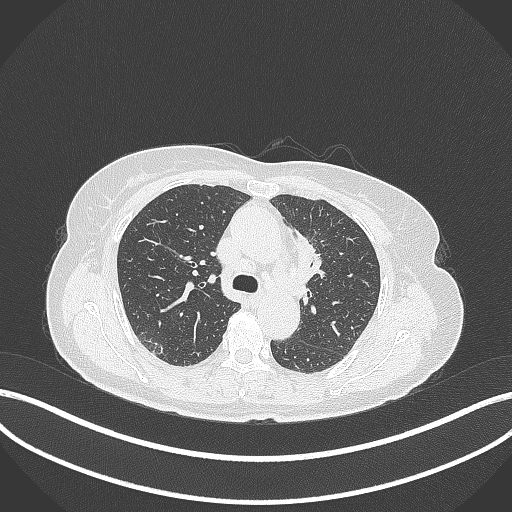
Chest CT, one axial slice. Slice 227 of 369 in the series (ordered by position). Lung window (W 1500 / L -600 HU). 1 mm slice thickness. 512 × 512 image matrix. Female patient, age 65 years. Case-level facts recorded for this patient, not image findings: clinical TNM (as recorded): T2a N0 M0; histopathological grade: G2-3.
Structures marked on this image (bounding box drawn by a radiologist):
- lung tumour (recorded histology: adenocarcinoma): box from (x=286, y=223) to (x=324, y=282) px